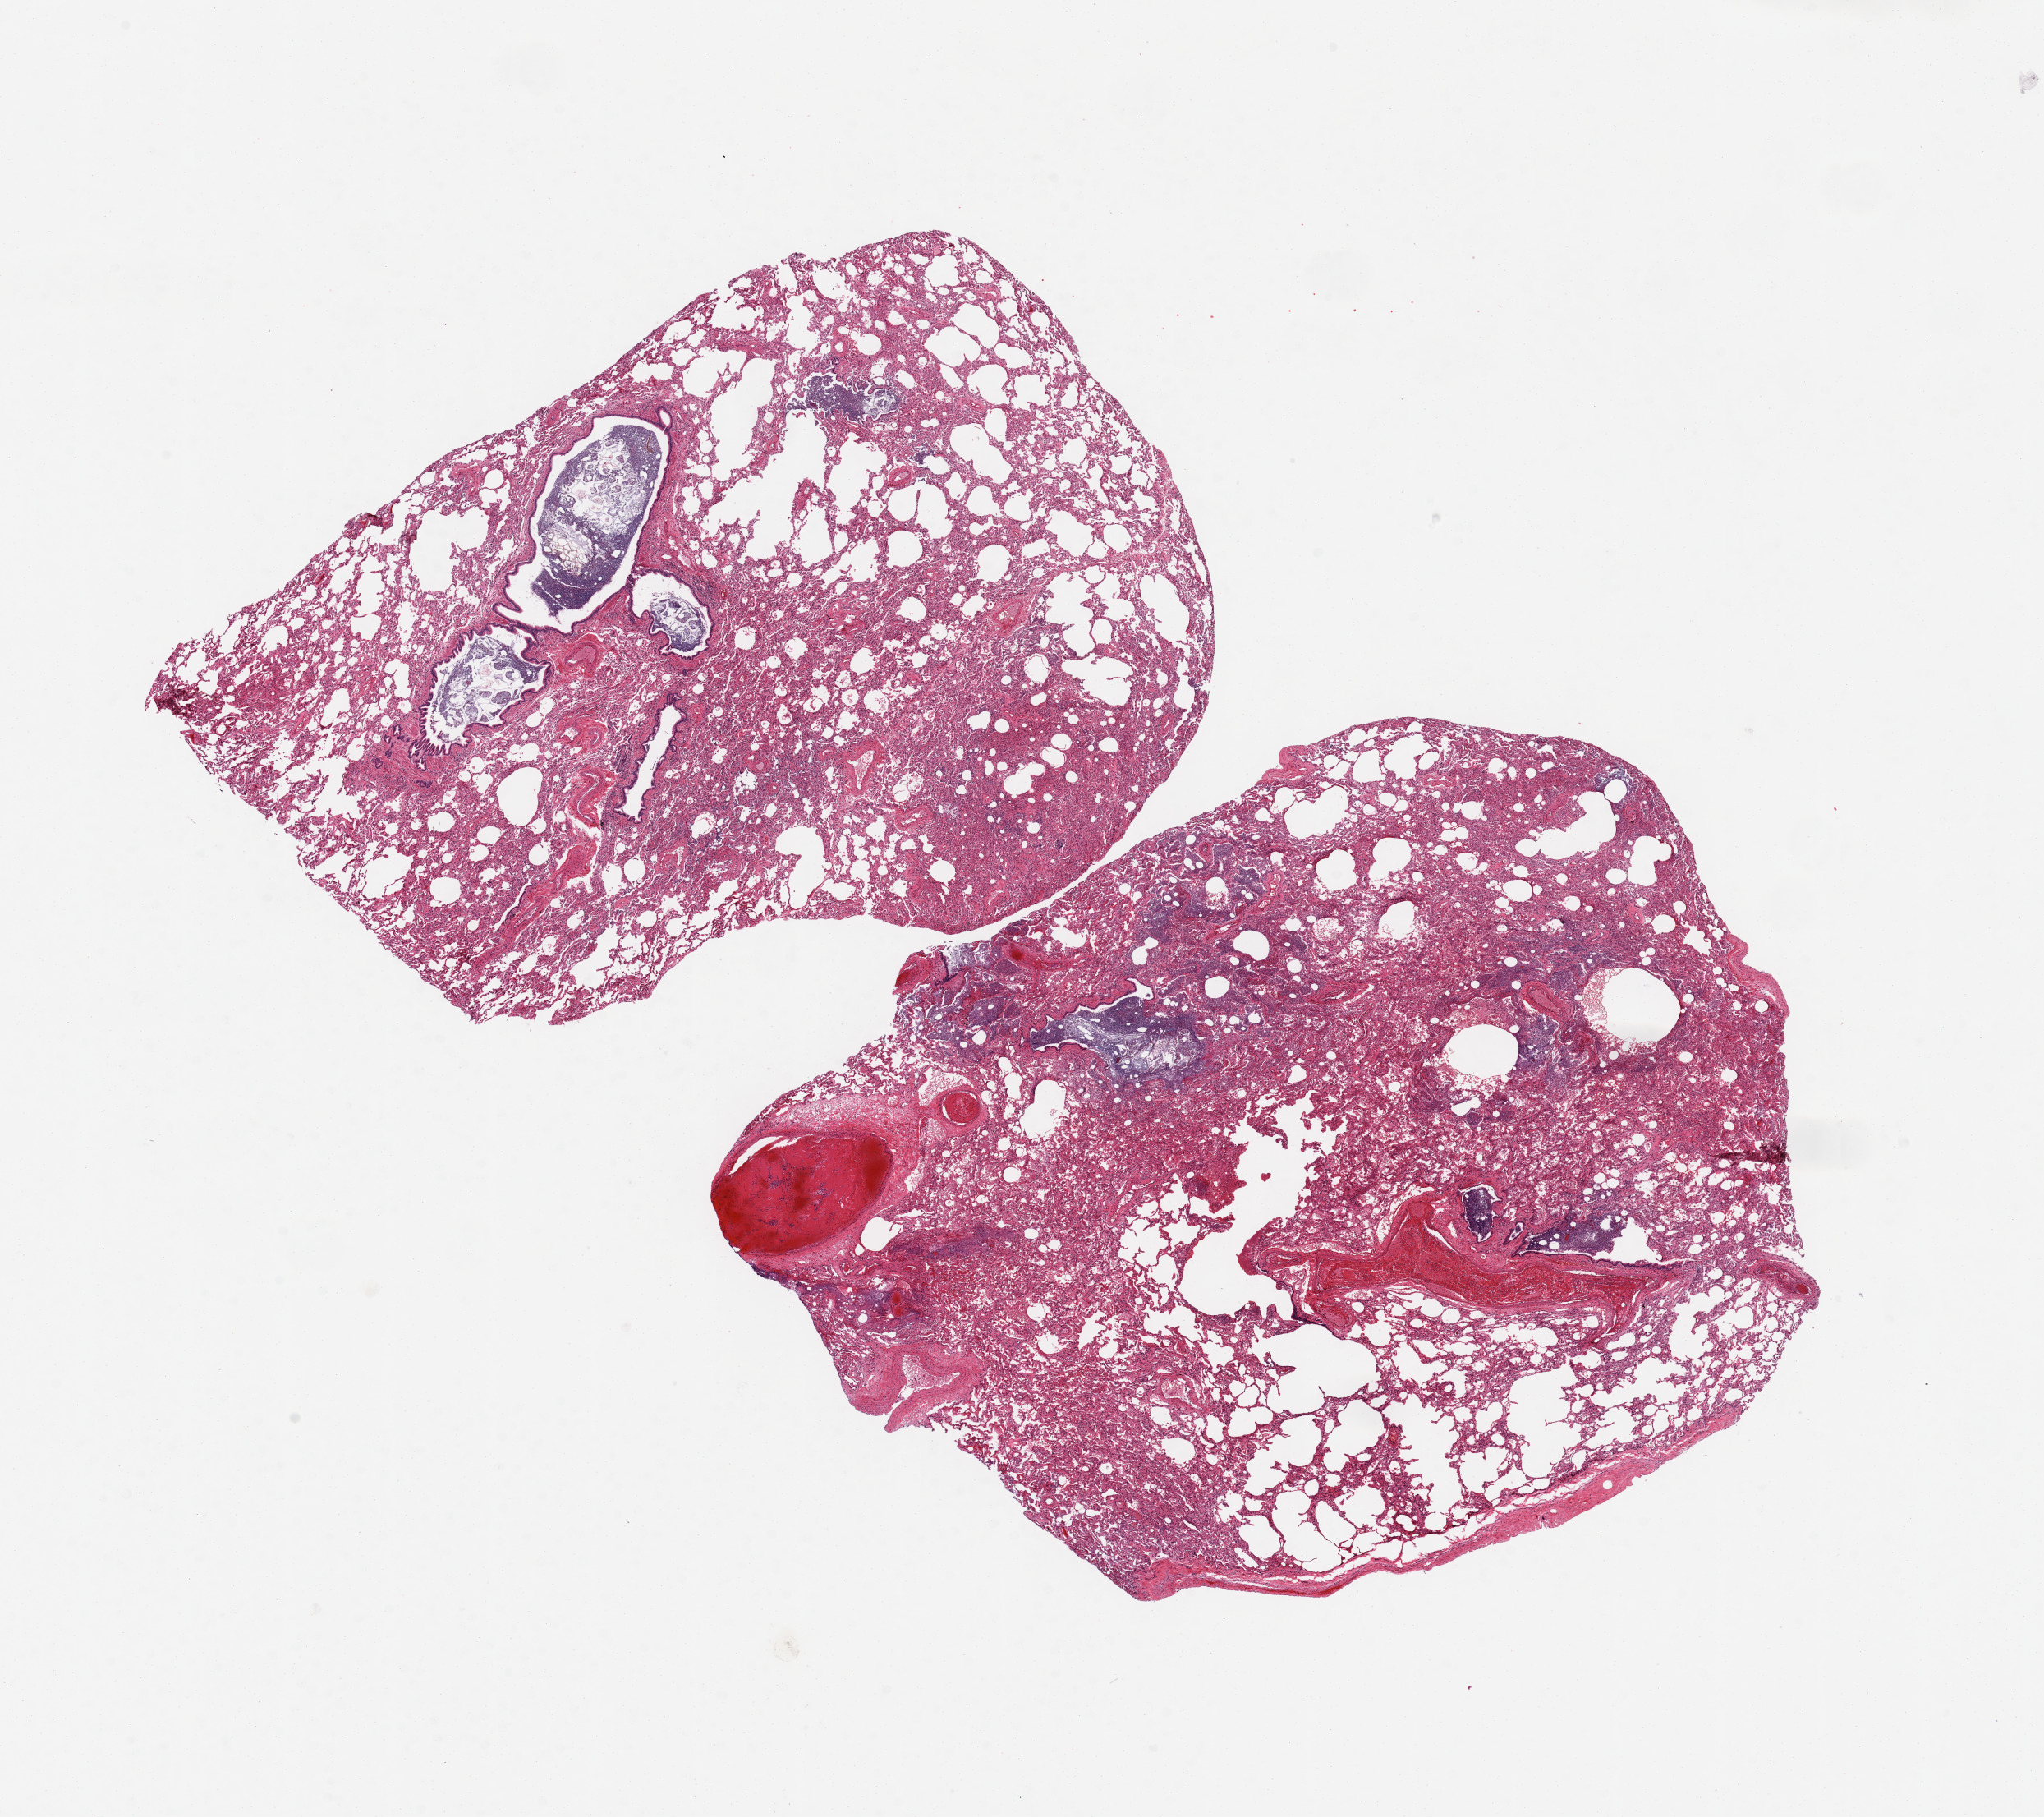
Whole-slide image, haematoxylin and eosin stain, low-resolution overview of the scanned area, about 19.7 x 17.5 mm (acquisition: 20x scan); PAXgene-fixed, paraffin-embedded tissue; target tissue: lung; tissue donor sample. Male donor.
- pathologist's review note for this sample: 2 pieces, ~9x8mm. Multiple foci of aspirated foreign material in dilated bronchi with acute infammation, patchy acute aspiration pneumonia in parenchyma